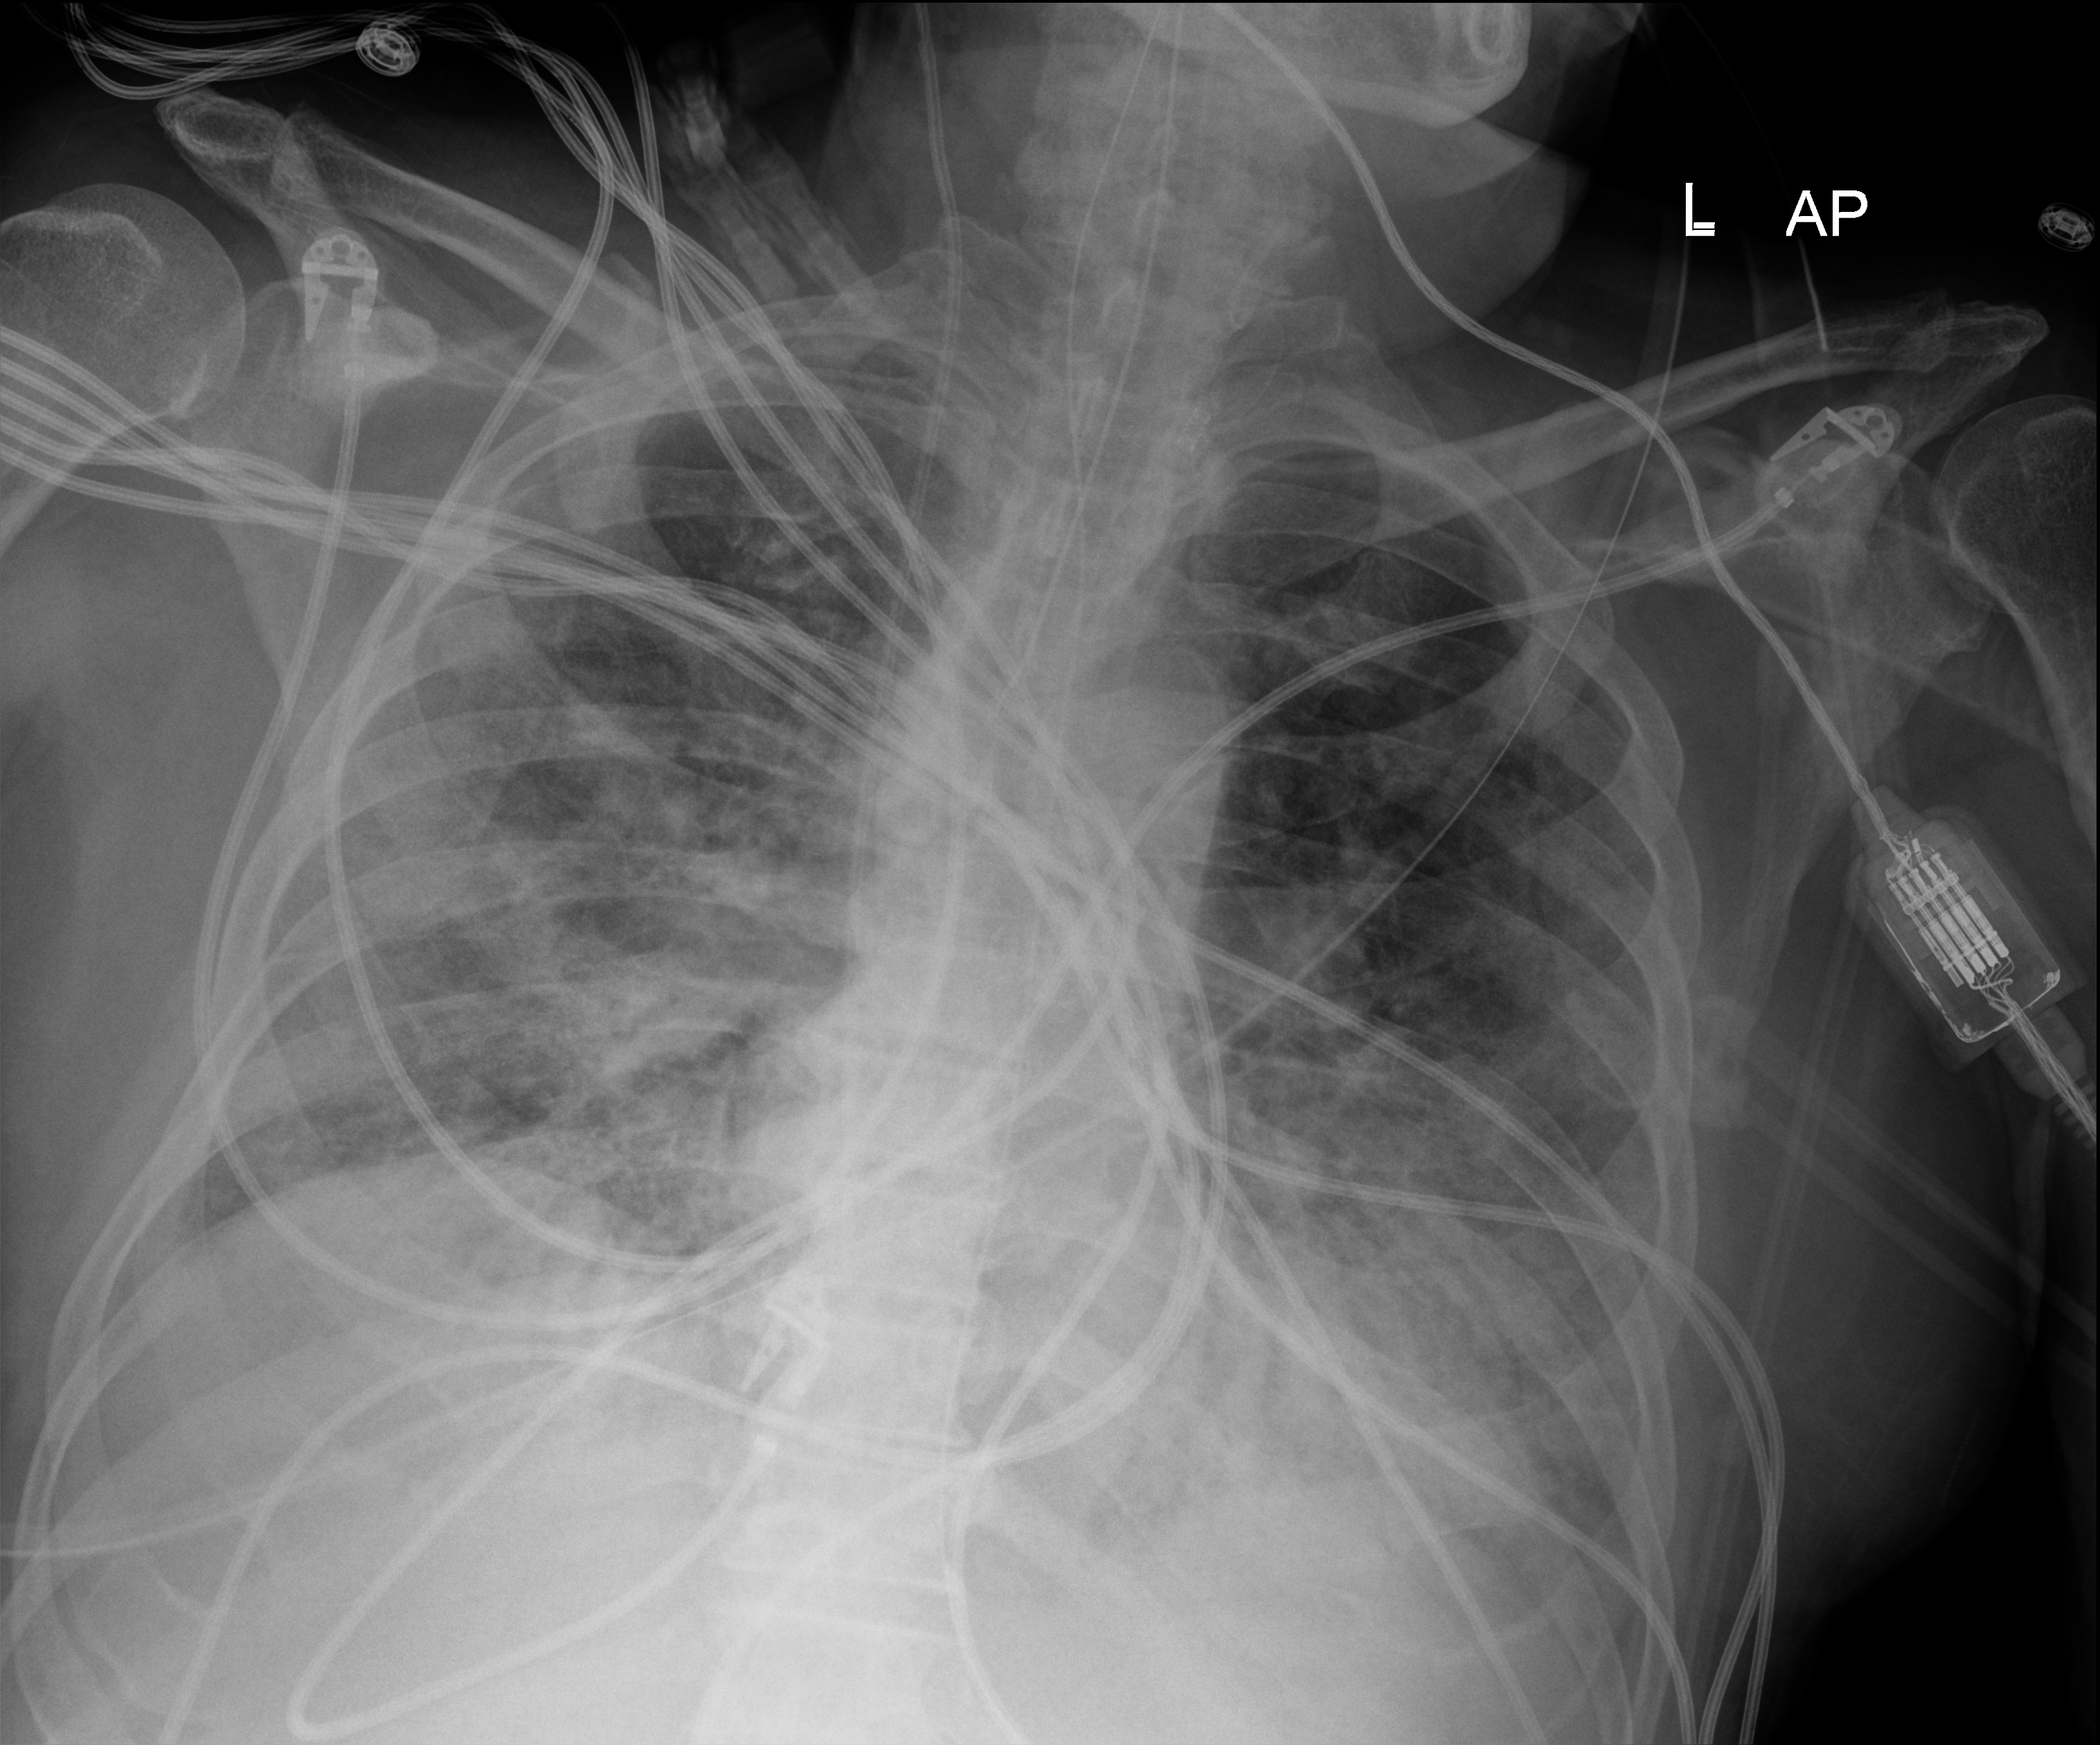
Portable chest radiograph; anteroposterior (AP) projection. Male patient hospitalised with COVID-19, age 75–90 years.
Admission-level facts for this patient (not findings on this image; timing relative to this image not recorded): hypertension (admission record): yes; admitted to intensive care during this hospital stay: yes; mechanically ventilated during this hospital stay: yes.